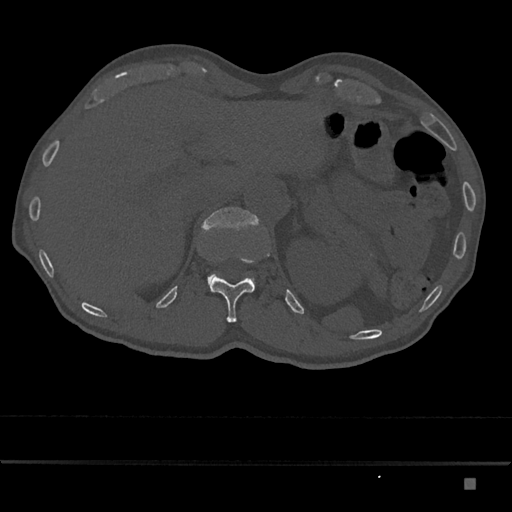
CT including the spine, one axial slice. Slice 593 of 797 in the series (ordered by position). 120 kVp. Bone window (W 1800 / L 400 HU). 512 × 512 image matrix, field of view 390 × 390 mm. Patient: male, 72 years. Case-level facts recorded for this patient, not image findings: primary cancer: prostate.
Outlined on this slice (semi-automatically segmented with operator editing):
- L1 vertebra: bounding box <201,207,261,290> (left, top, right, bottom; pixels)
- T12 vertebra: <210,258,254,323>